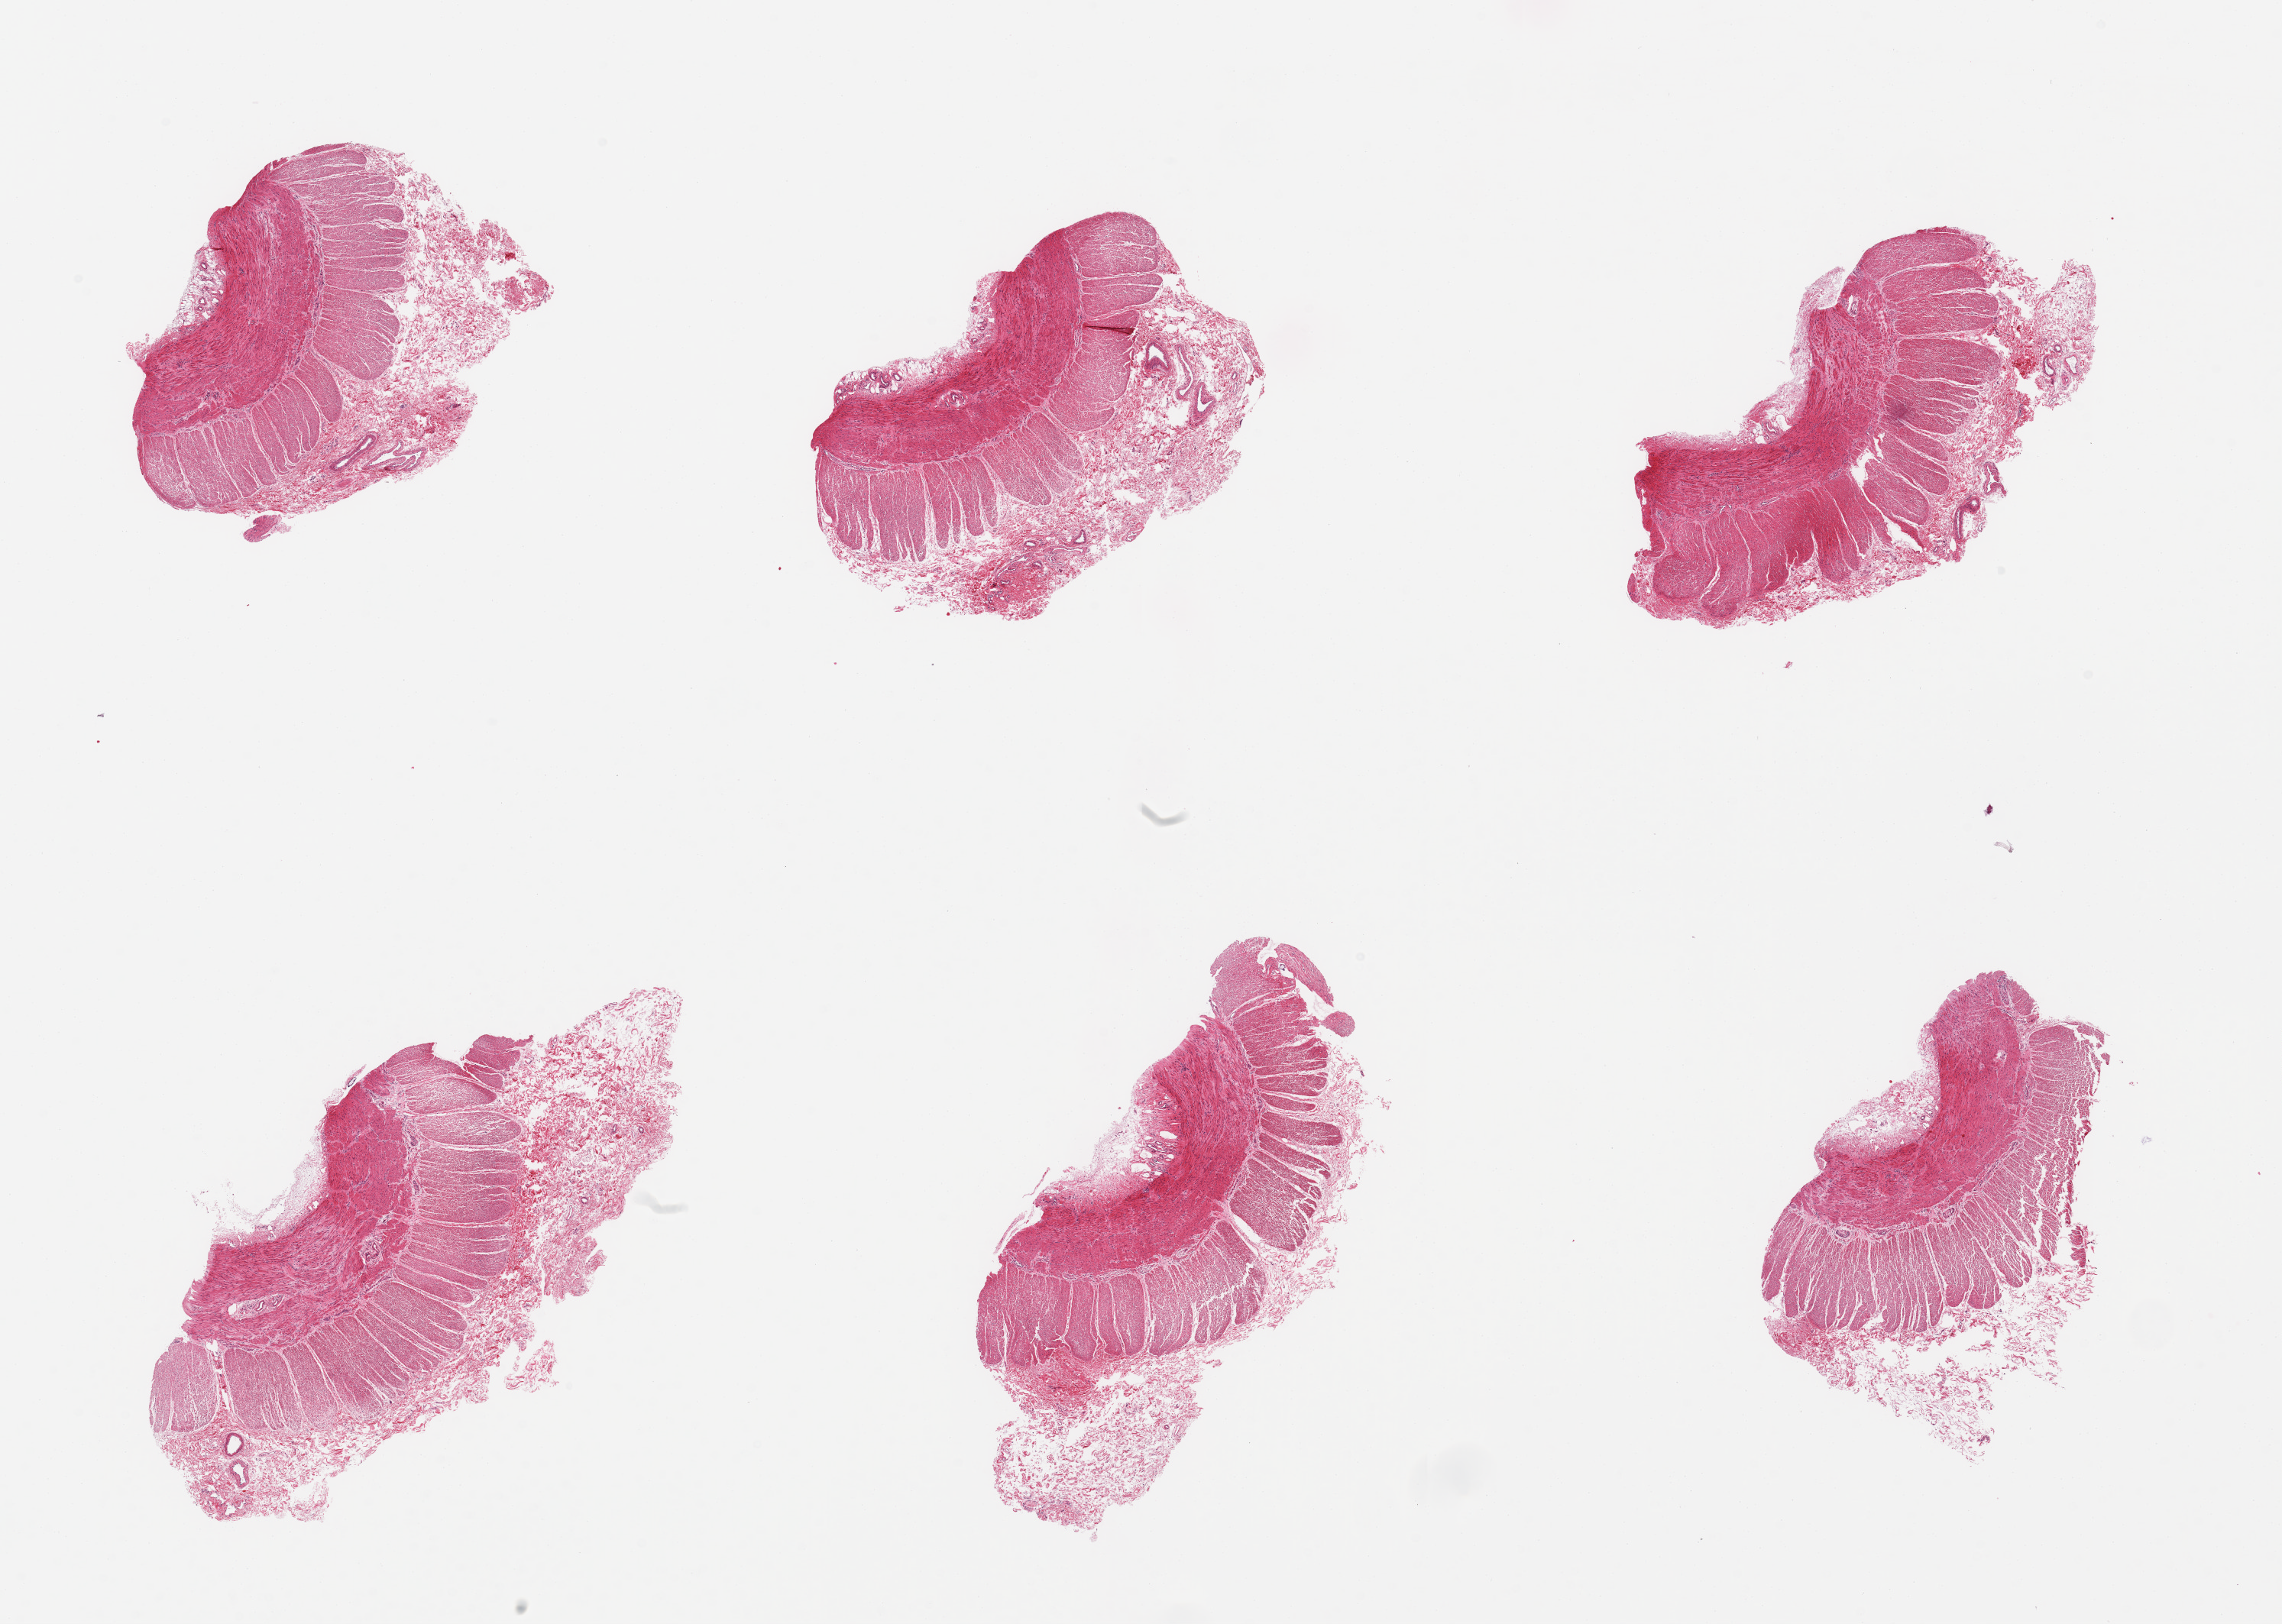
Whole-slide image, hematoxylin and eosin (H&E) stain — shown as a low-resolution overview of the whole scanned area (about 23.6 x 16.8 mm, slide scanned at 20x), PAXgene-fixed, paraffin-embedded tissue, sampled site (target tissue): transverse colon, donor tissue sample.
- reviewer comment on this tissue sample: 6 pieces; all have muscle, but no mucosa